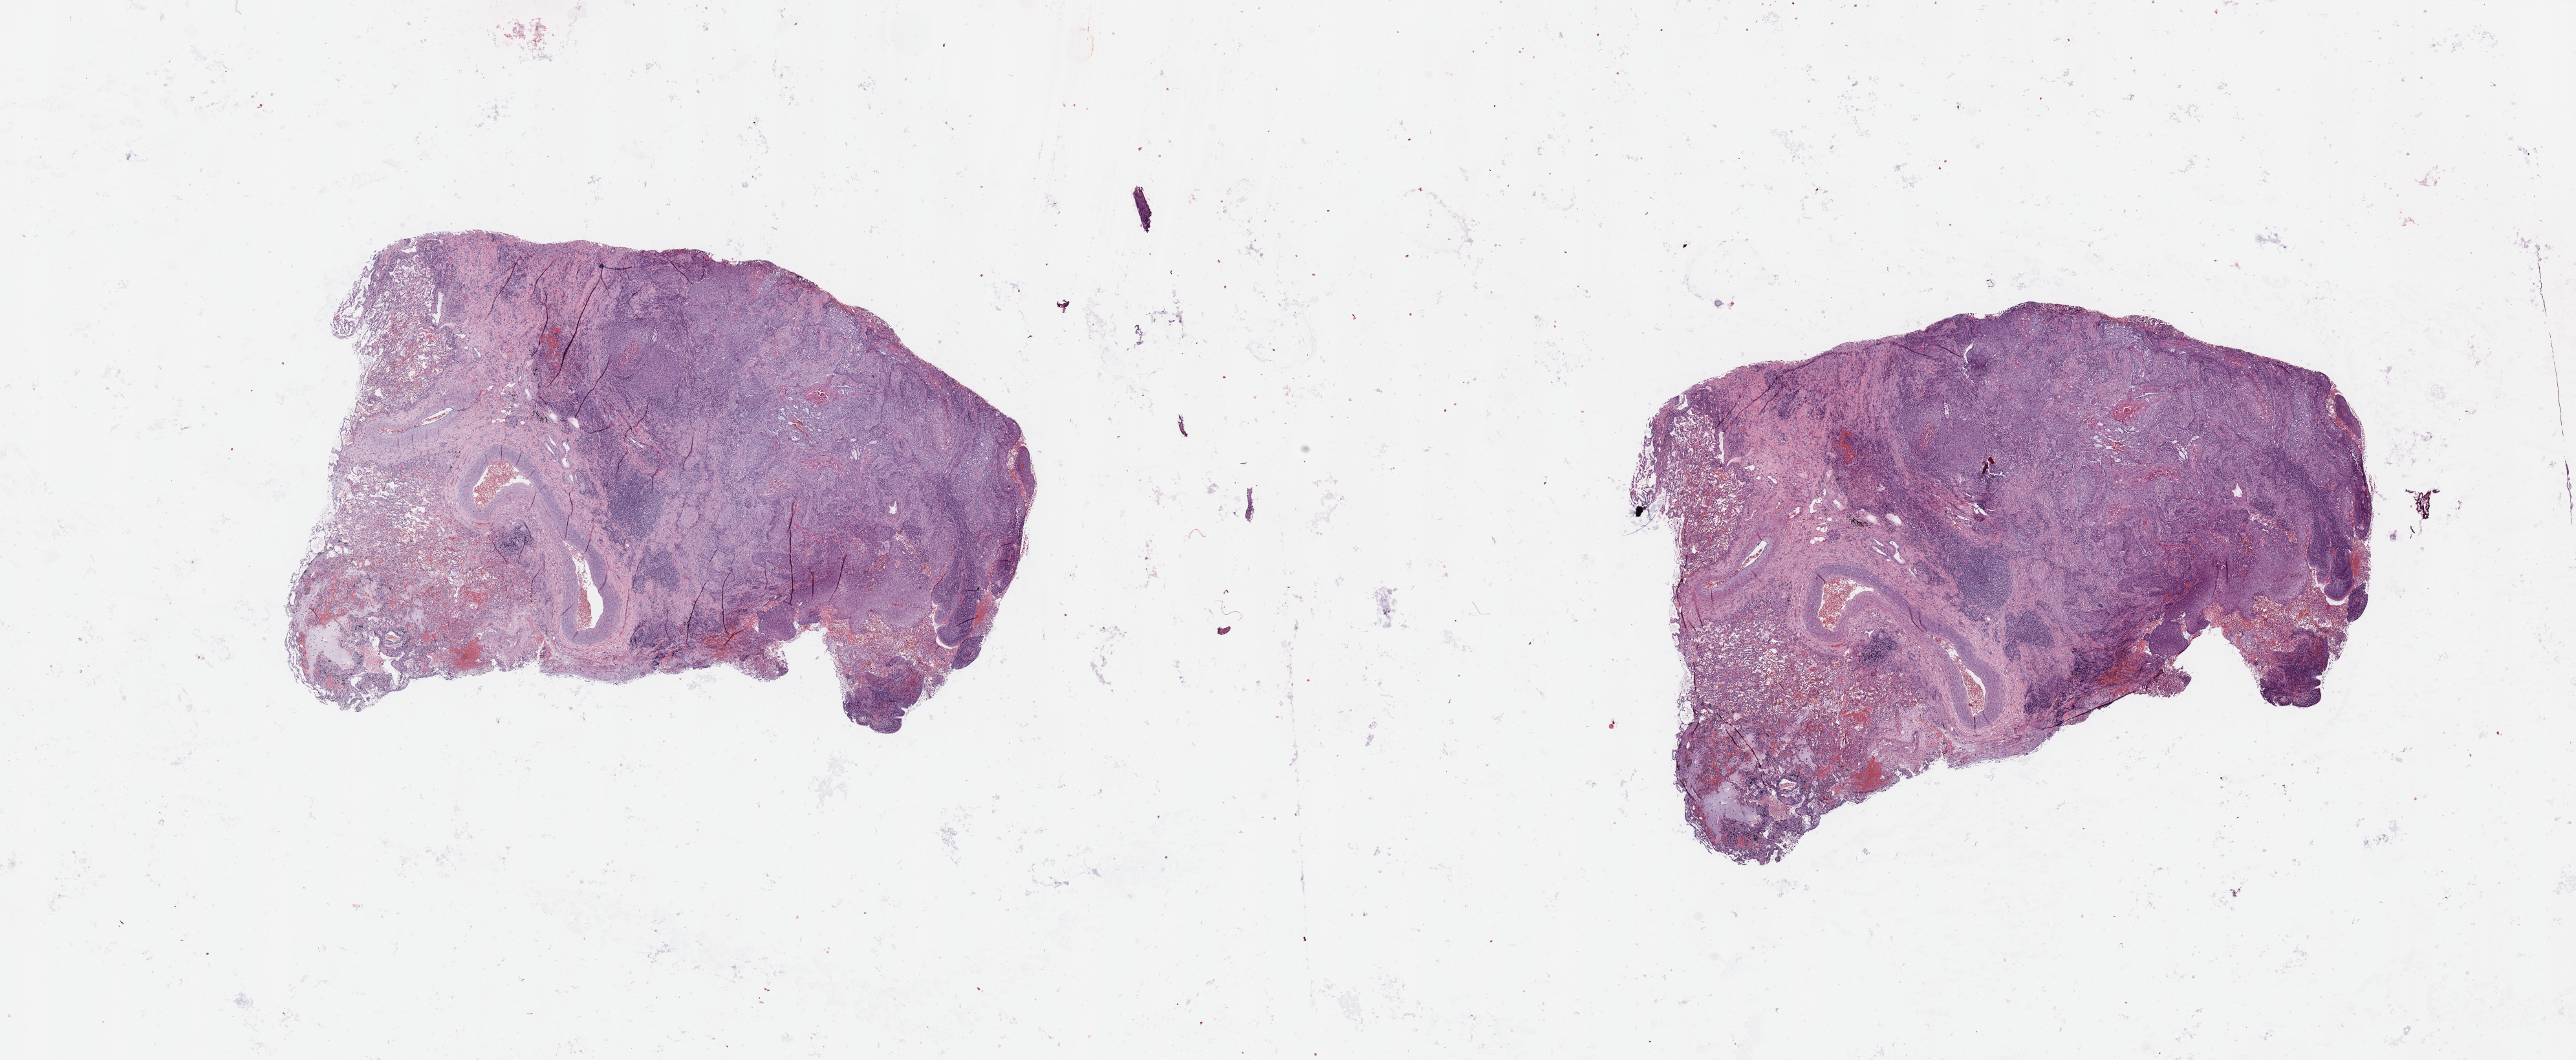
Digitized H&E tissue section (whole slide) — whole scanned area (about 31.5 x 13.0 mm) shown as a low-resolution overview. Lung, tumour tissue. 48-year-old female patient. Histologic grade: G2 (moderately differentiated).
• primary tumour site (as recorded): left upper lobe
• histologic diagnosis: Squamous cell carcinoma, NOS
• AJCC pathologic stage: IB